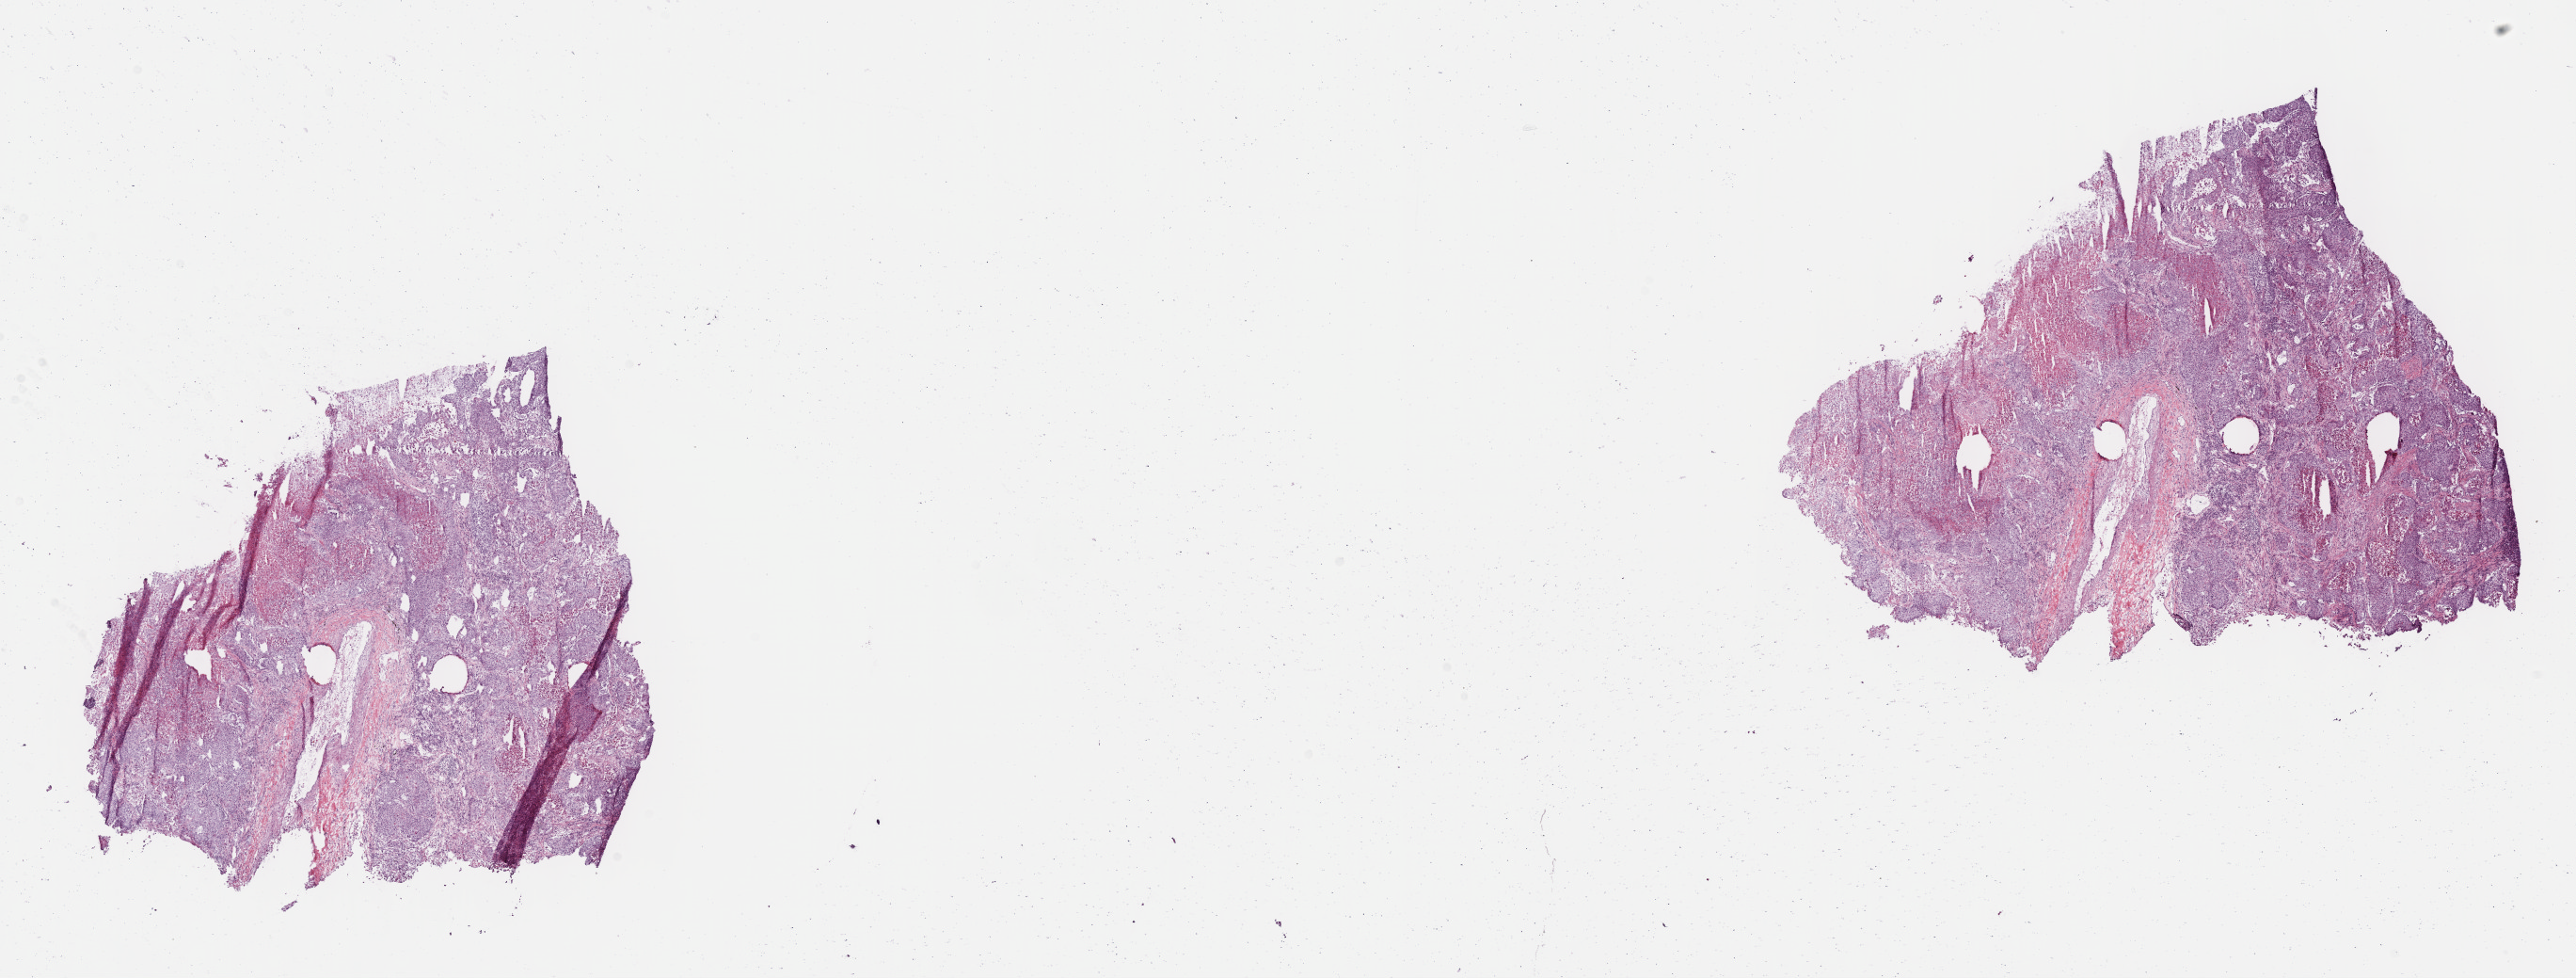
H&E whole-slide image — low-resolution overview of the scanned area, about 22.1 x 8.4 mm, frozen section from the top of the tissue portion, sample: primary tumour, lung. Male patient; age at initial diagnosis 64 years. Pathologist review of this section (percent, as recorded): tumour cells 70%, tumour nuclei 80%, normal cells 0%, stromal cells 10%, necrosis 20%. Infiltration values recorded for this section: lymphocyte infiltration 5%, monocyte infiltration 0%, neutrophil infiltration 5%.
Diagnosis: Squamous cell carcinoma, NOS (upper lobe, lung). AJCC pathologic stage: IIB (7th edition).